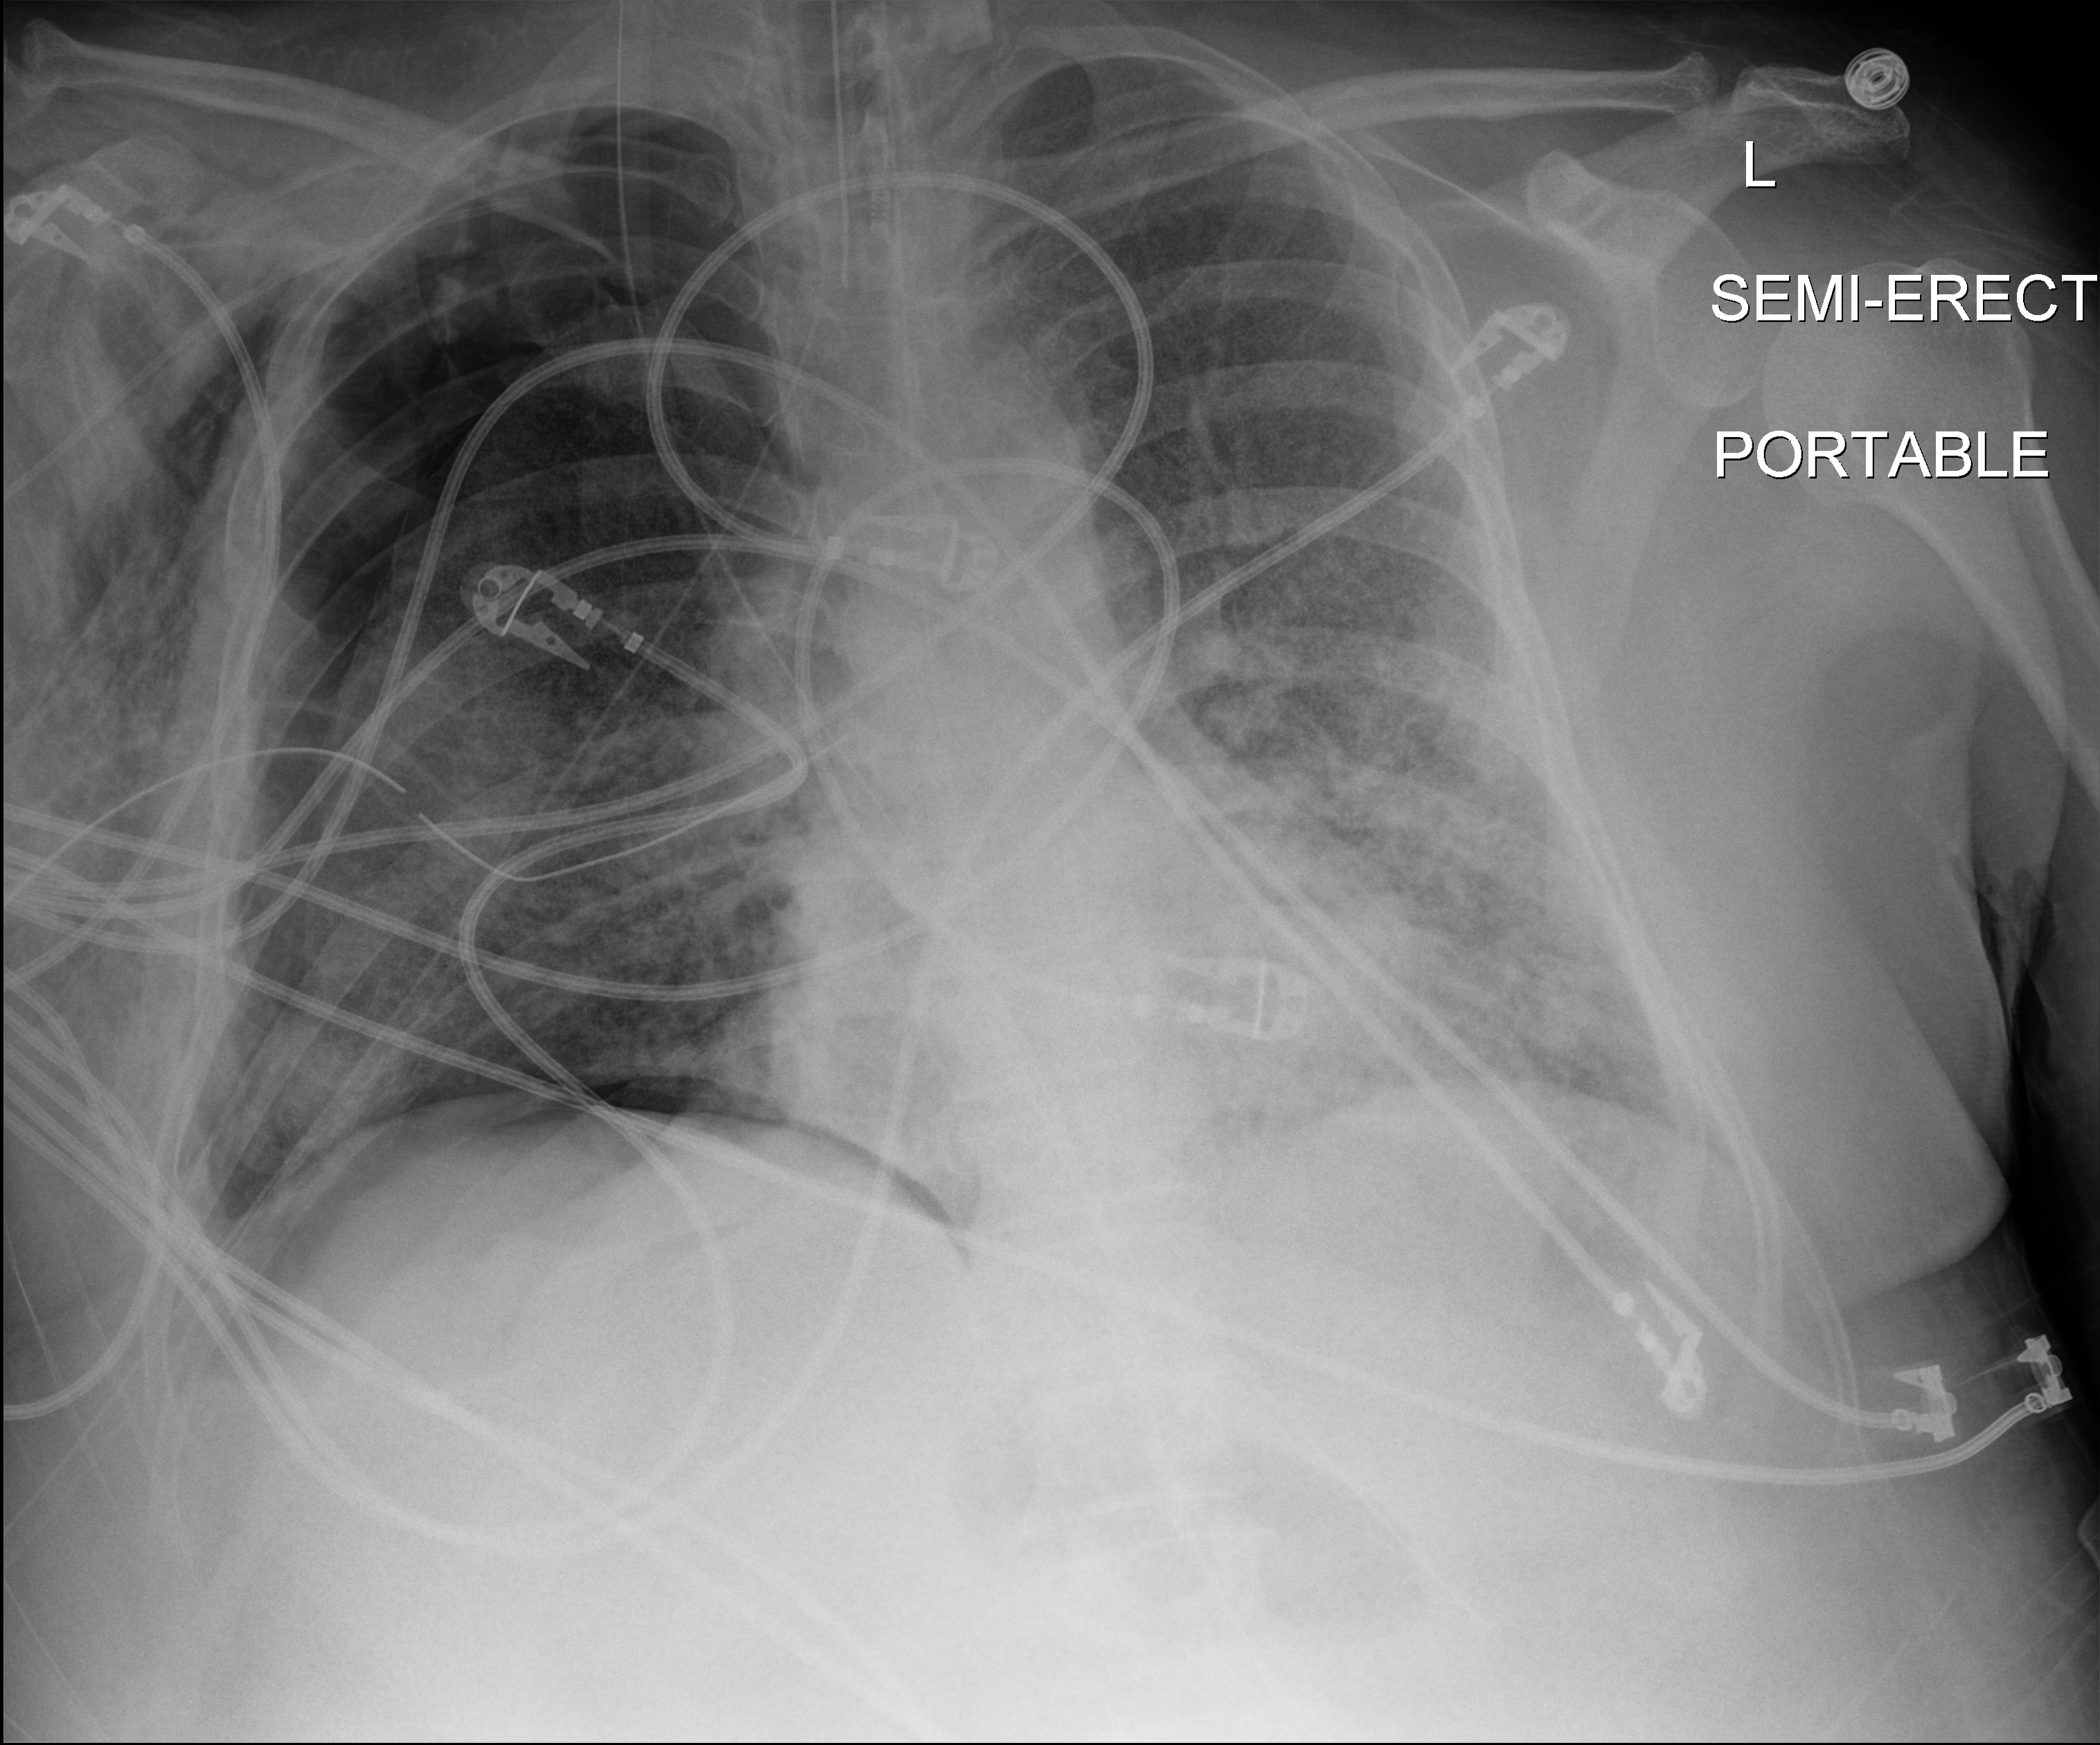
Chest X-ray (portable); anteroposterior (AP) projection. Patient hospitalised with COVID-19, aged 18–59 years.
Hospital-stay facts (about this admission, not read from this image; timing relative to this image not recorded): mechanically ventilated during this hospital stay: yes.